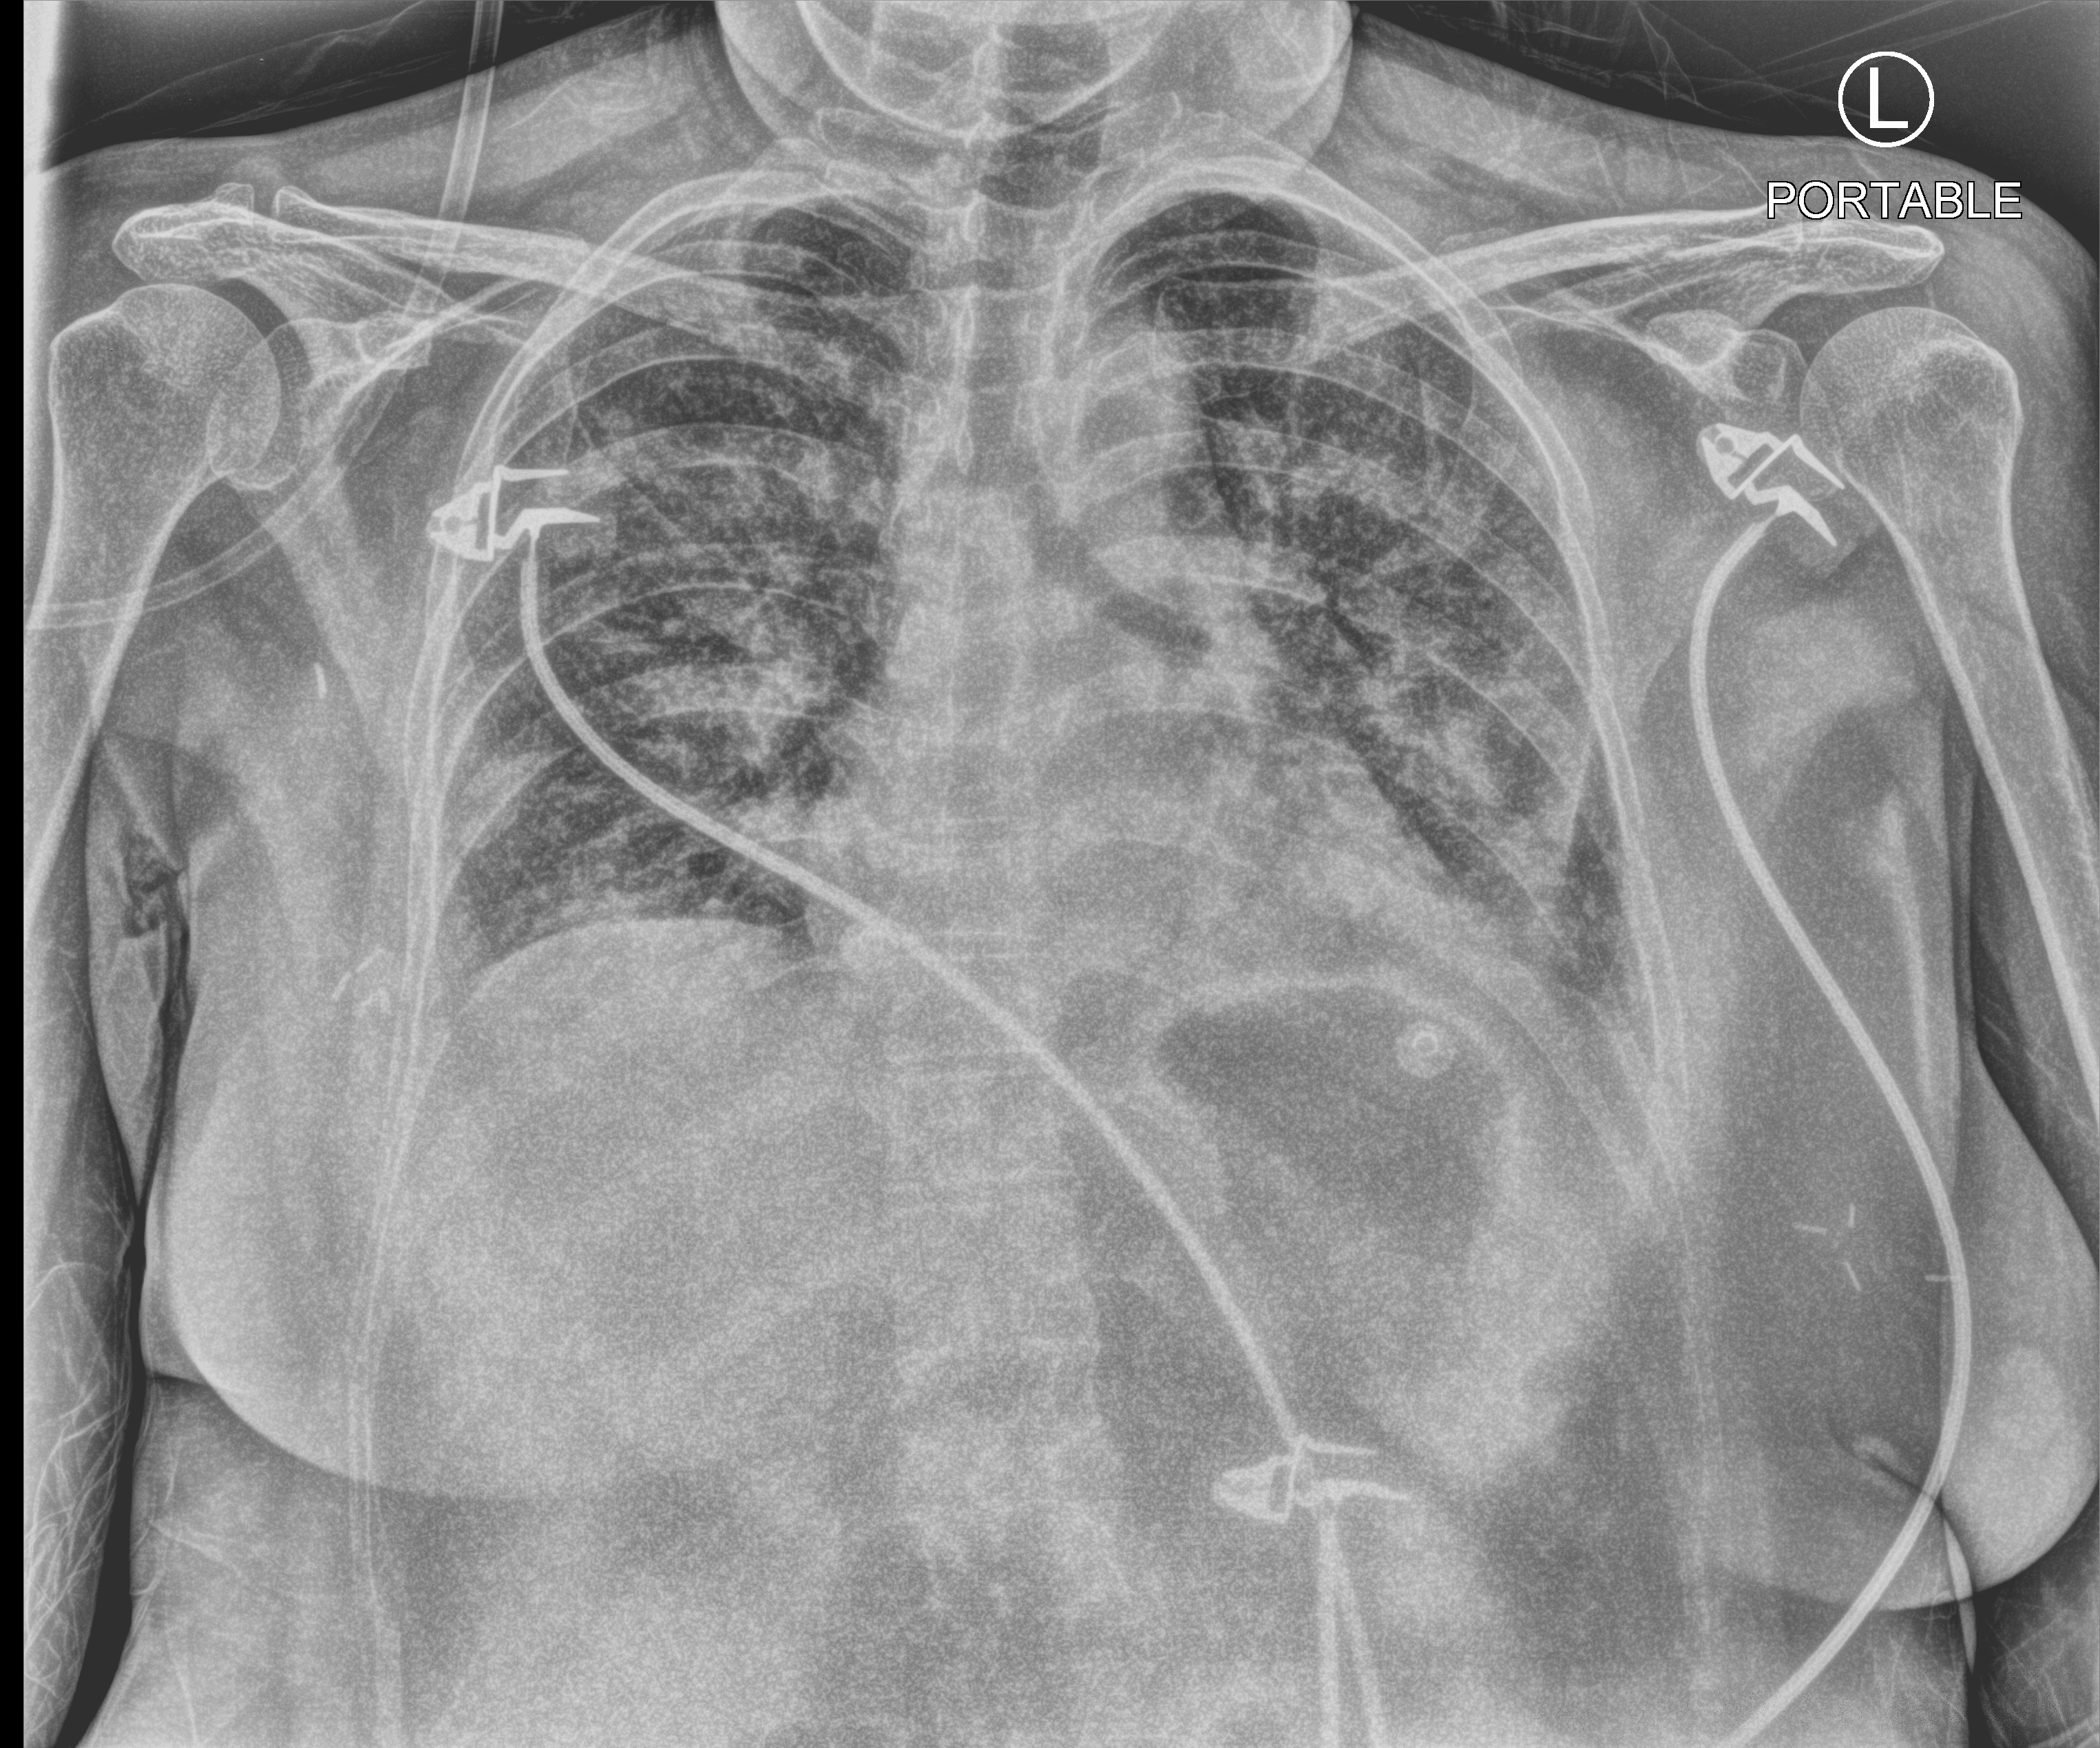
Chest X-ray (portable), anteroposterior (AP) projection. Female patient hospitalised with COVID-19, age 18–59 years.
Admission-level facts for this patient (not findings on this image; timing relative to this image not recorded):
- admitted to intensive care during this hospital stay: no
- length of hospital stay: 21 days
- mechanically ventilated during this hospital stay: yes